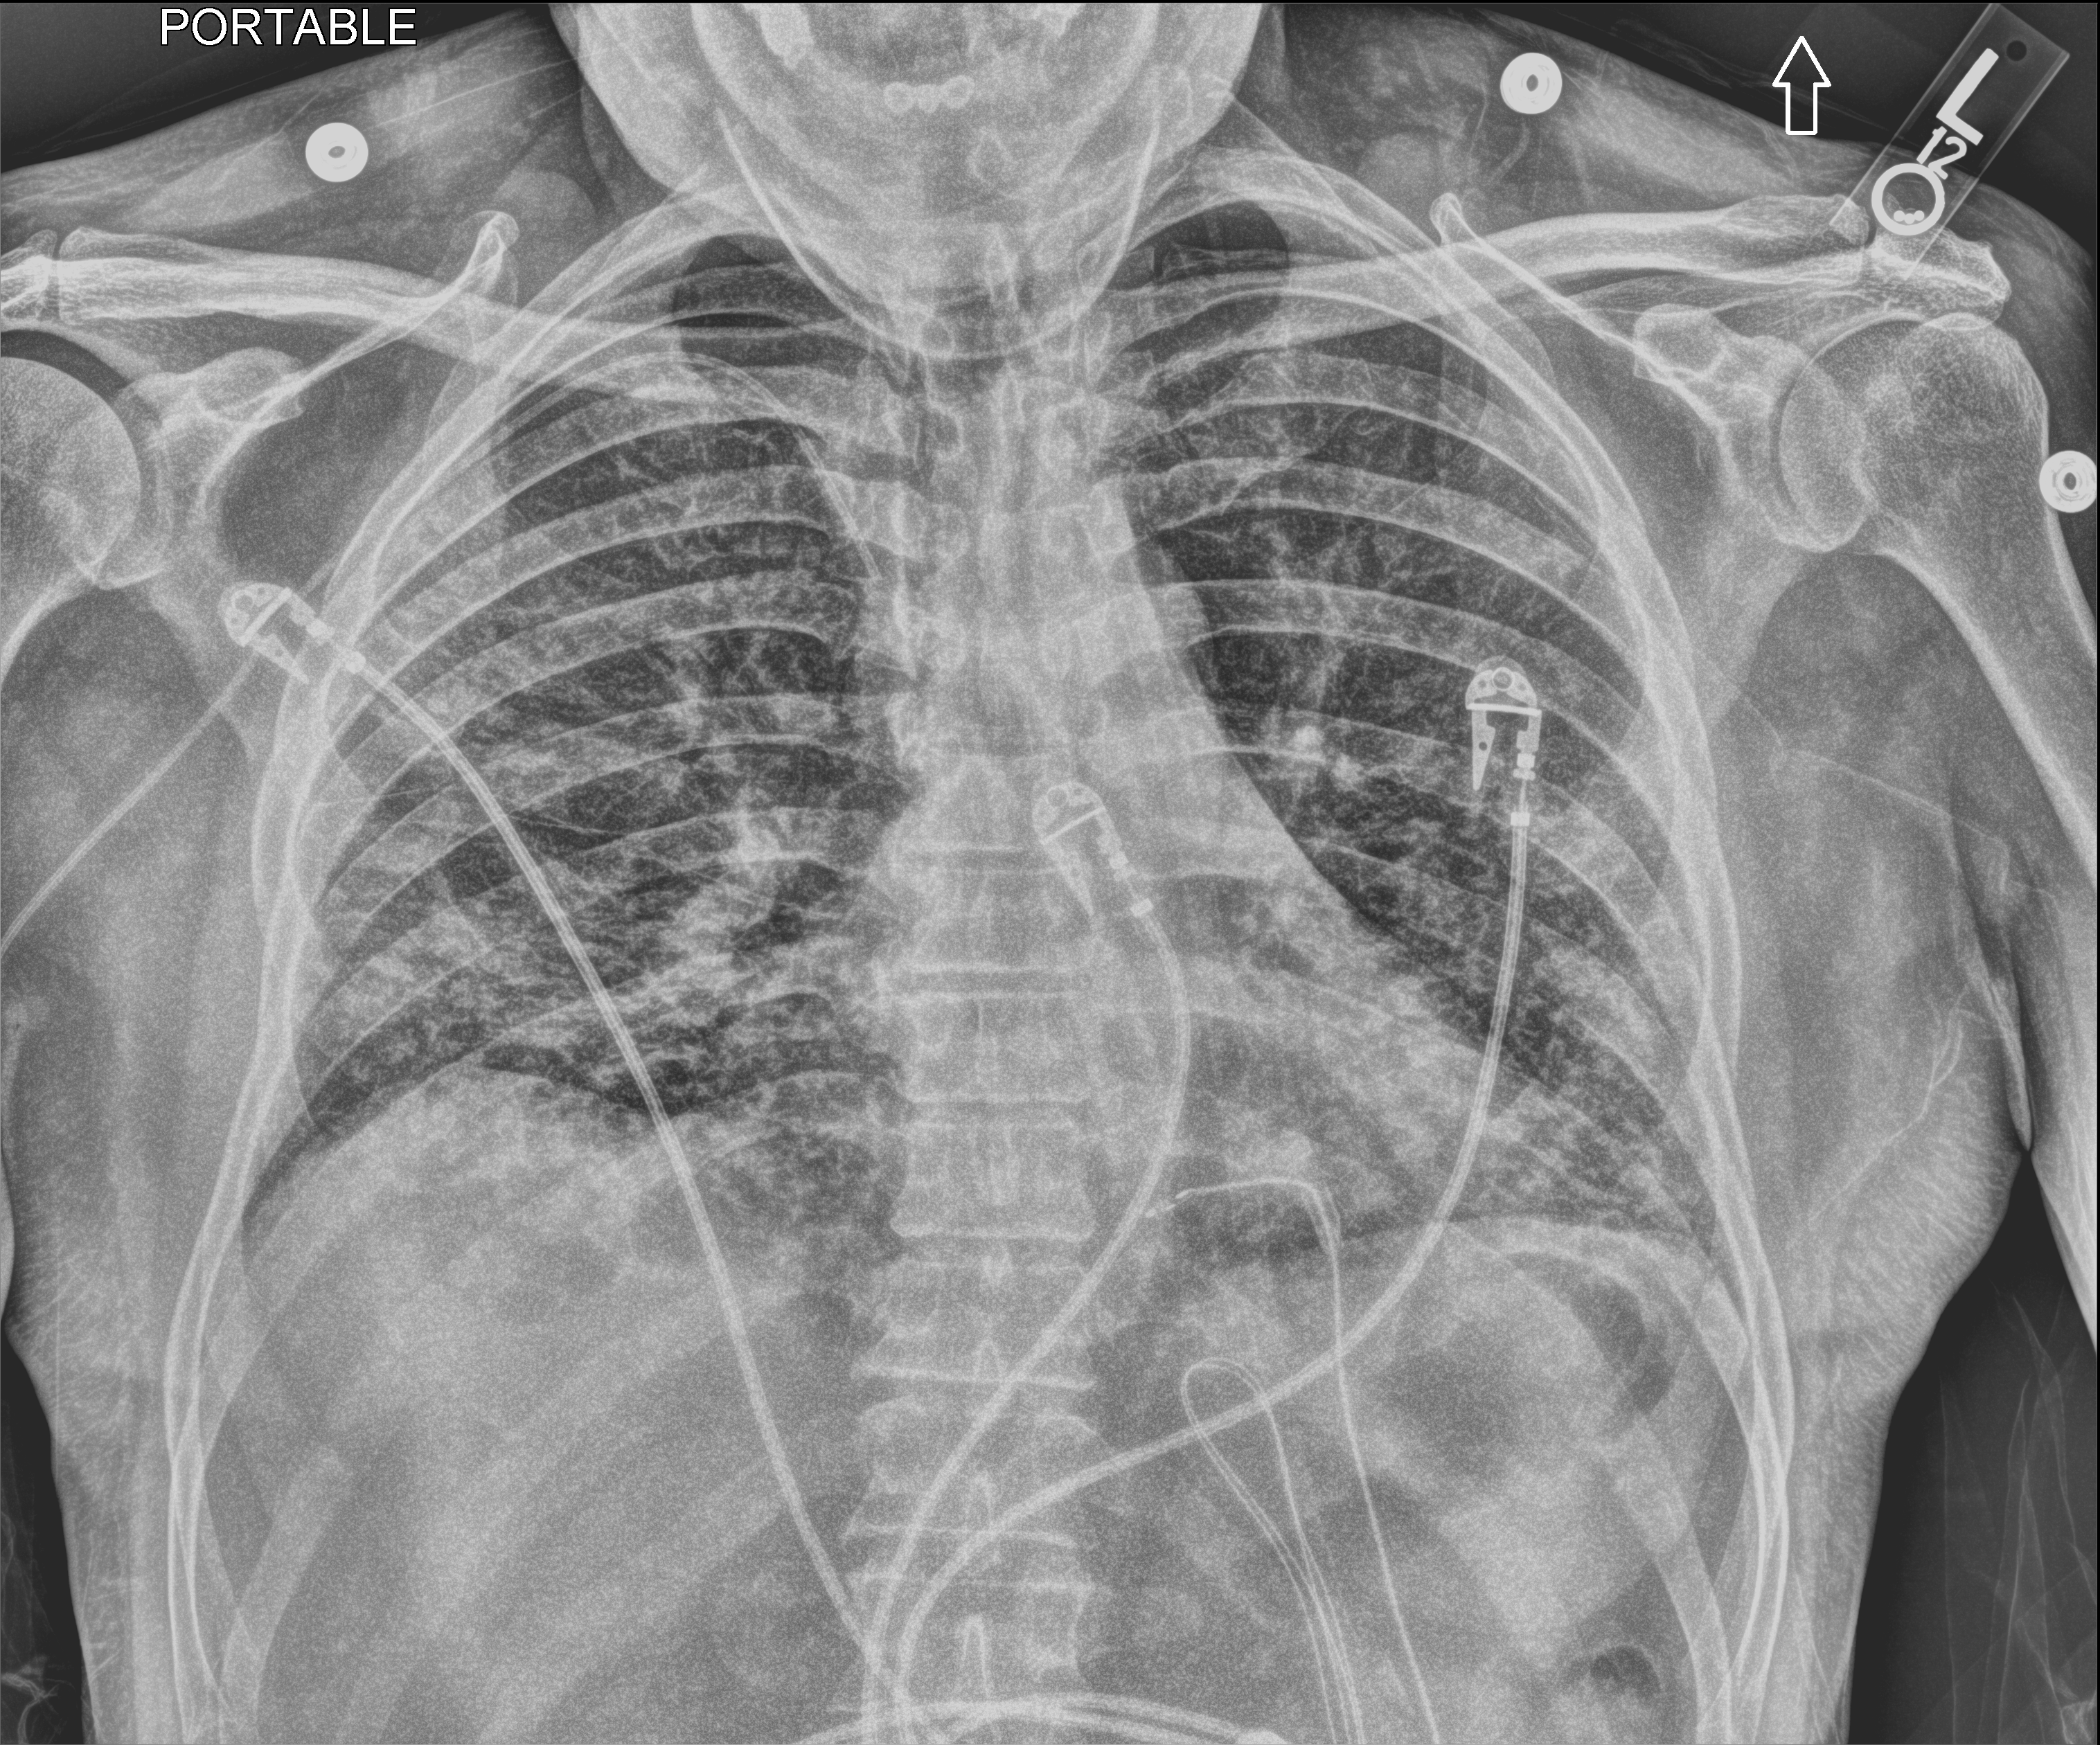
Chest X-ray (portable), anteroposterior (AP) projection. Patient hospitalised with COVID-19; male, aged 18–59 years.
From the hospital-stay record, not from the radiograph (when in the stay this image was taken is not recorded): mechanically ventilated during this hospital stay: no; chronic kidney disease (admission record): no; admitted to intensive care during this hospital stay: yes.